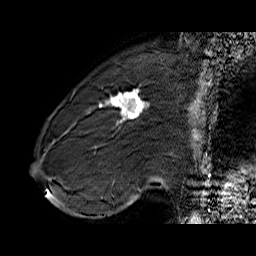
Breast MRI (dynamic contrast-enhanced), one sagittal slice; position 18 of 60 along the scan axis; dynamic contrast-enhanced series, time point 2 of 6 at this slice position (early post-contrast); 1.5 T; TE 6.4 ms, TR 32.9 ms; 4 mm slice thickness; 256 × 256 image matrix, field of view 200 × 200 mm. Female patient. Case-level facts recorded for this patient, not image findings: setting: breast cancer imaged before/during neoadjuvant chemotherapy; receptor status: HER2-positive.
Outlined on this slice (semi-automatically segmented with operator editing):
- analysis volume of interest (the breast-tissue region the enhancement analysis was run in; not a lesion): box from (x=71, y=80) to (x=155, y=146) px
- tumour enhancement mask (voxels above the 100 % enhancement threshold inside the analysis volume of interest): (x=99, y=89)–(x=149, y=124)